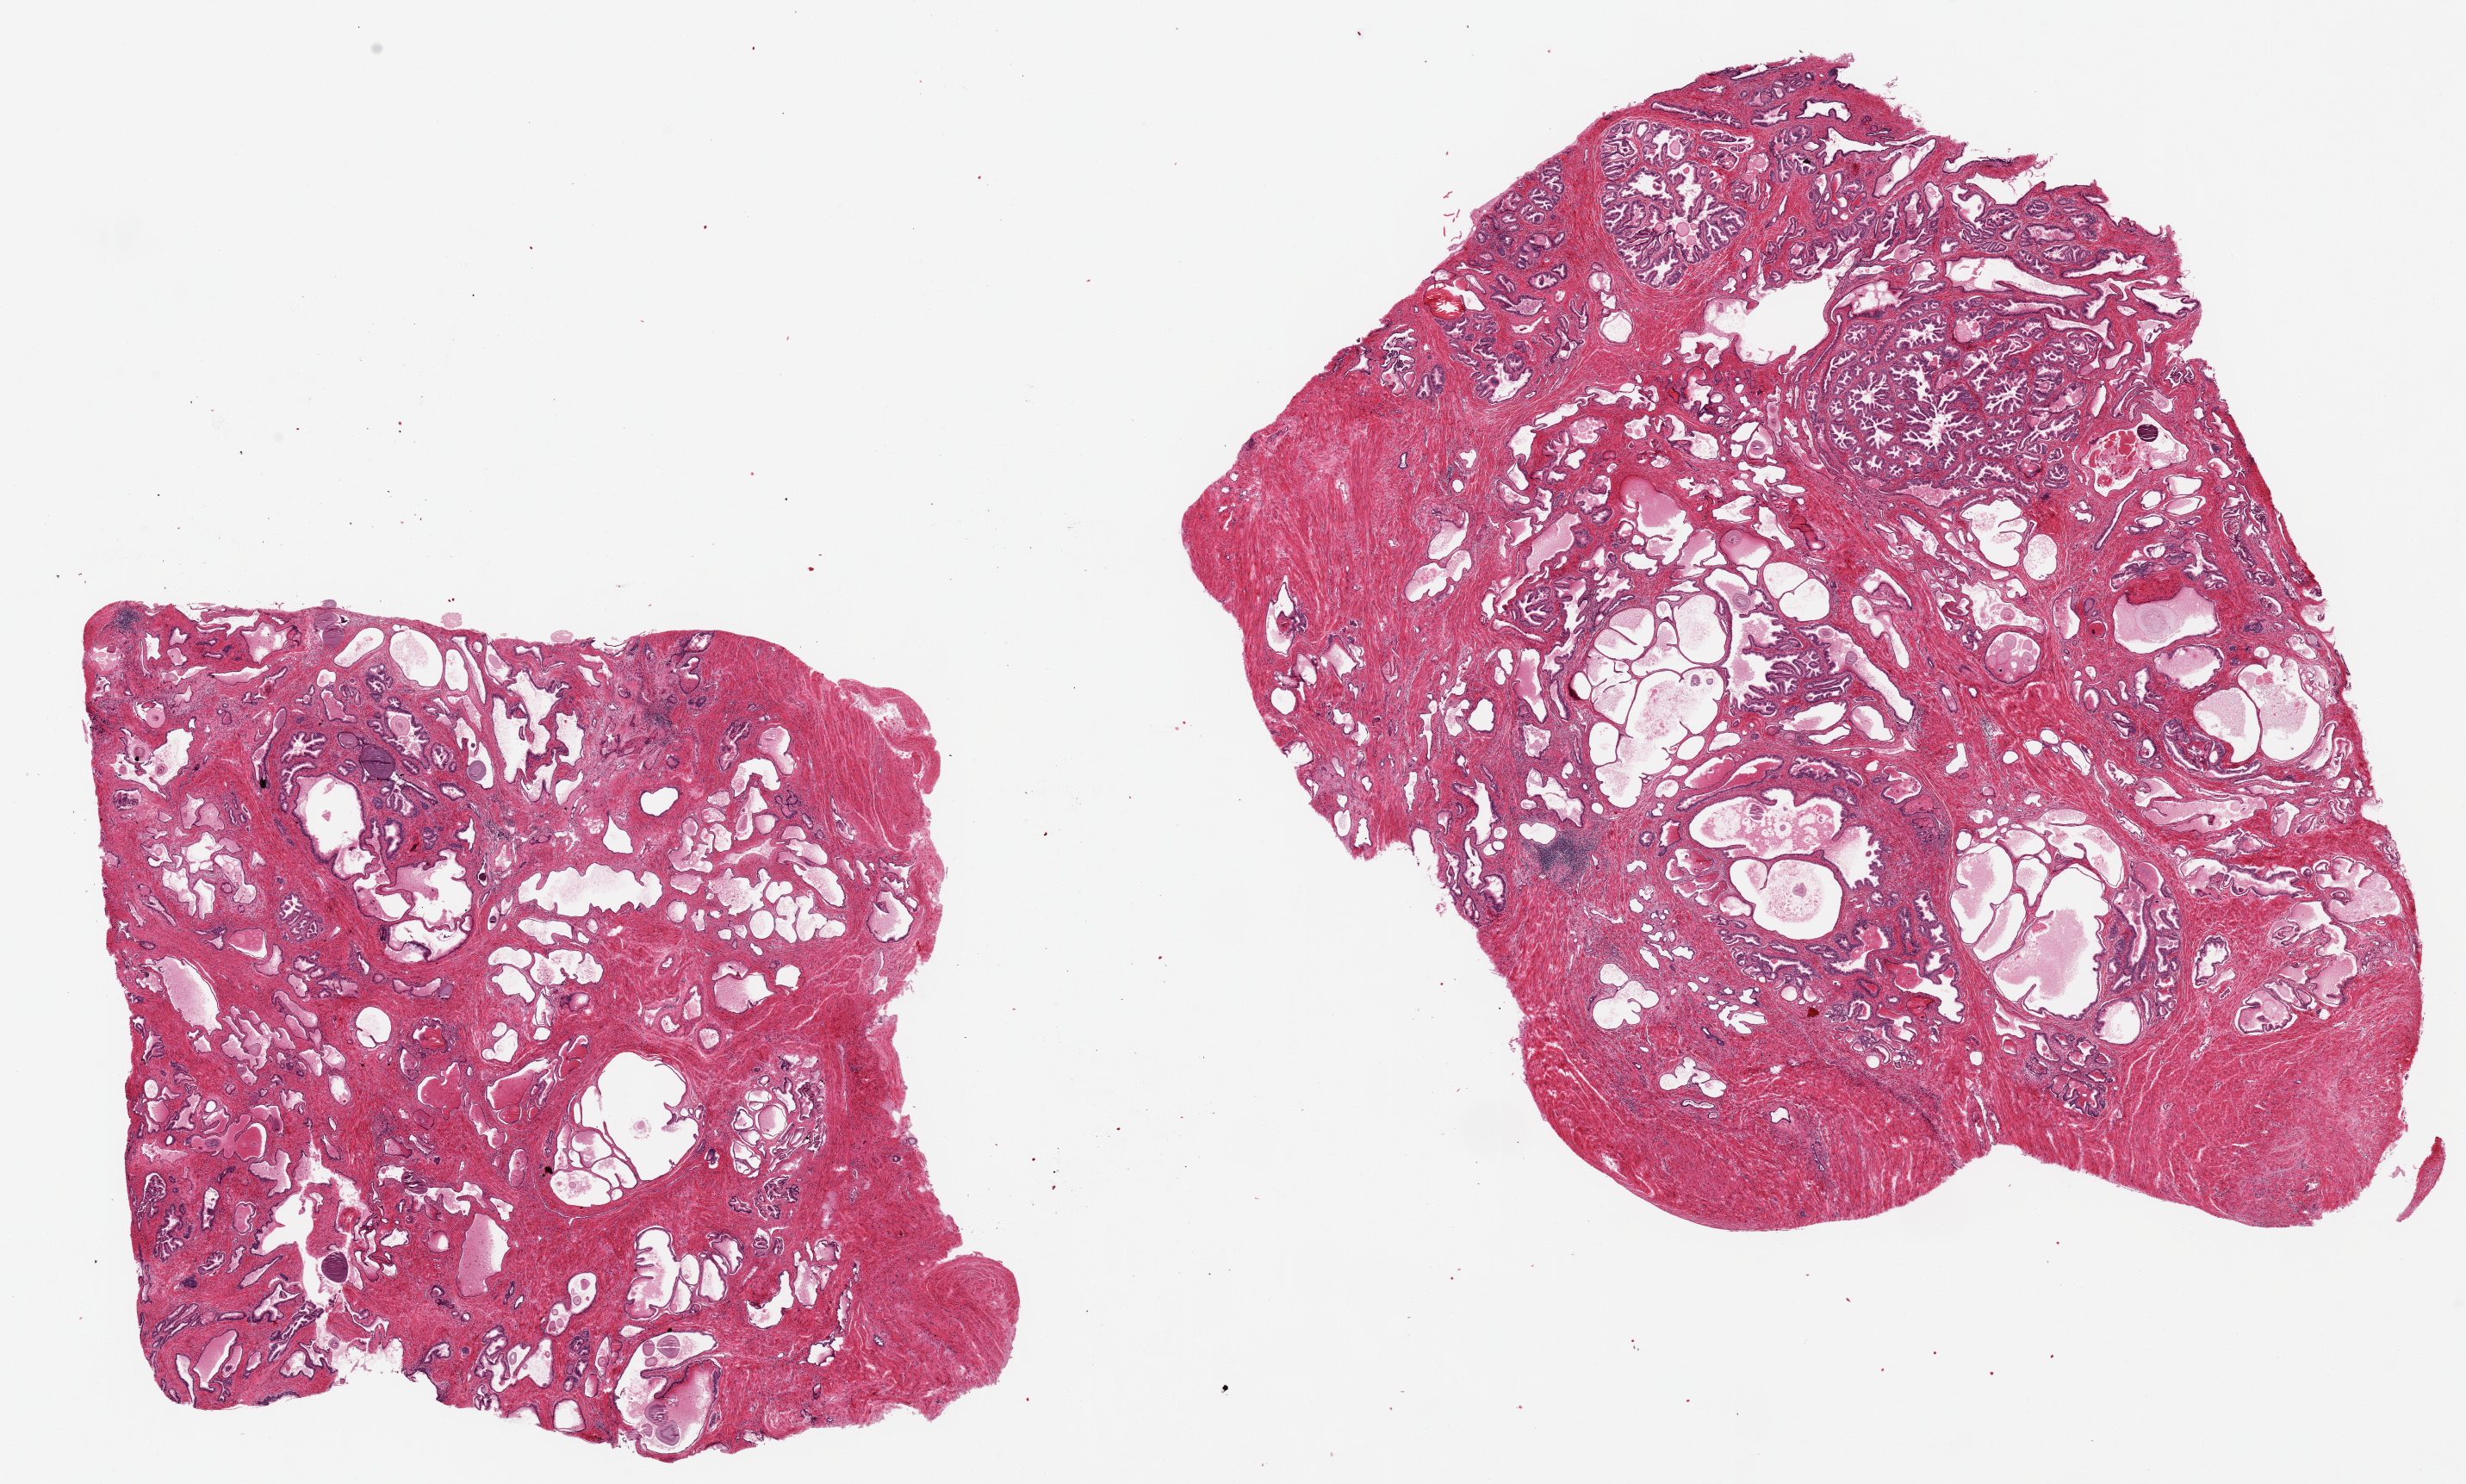
Hematoxylin and eosin (H&E) whole-slide image — whole scanned area (about 22.6 x 13.6 mm) shown as a low-resolution overview, PAXgene-fixed, paraffin-embedded tissue, target tissue: prostate, tissue donor sample. Donor sex: male.
- review note (as recorded): 2 pieces 12x8&8x7 mm; hyperplasia and atrophy